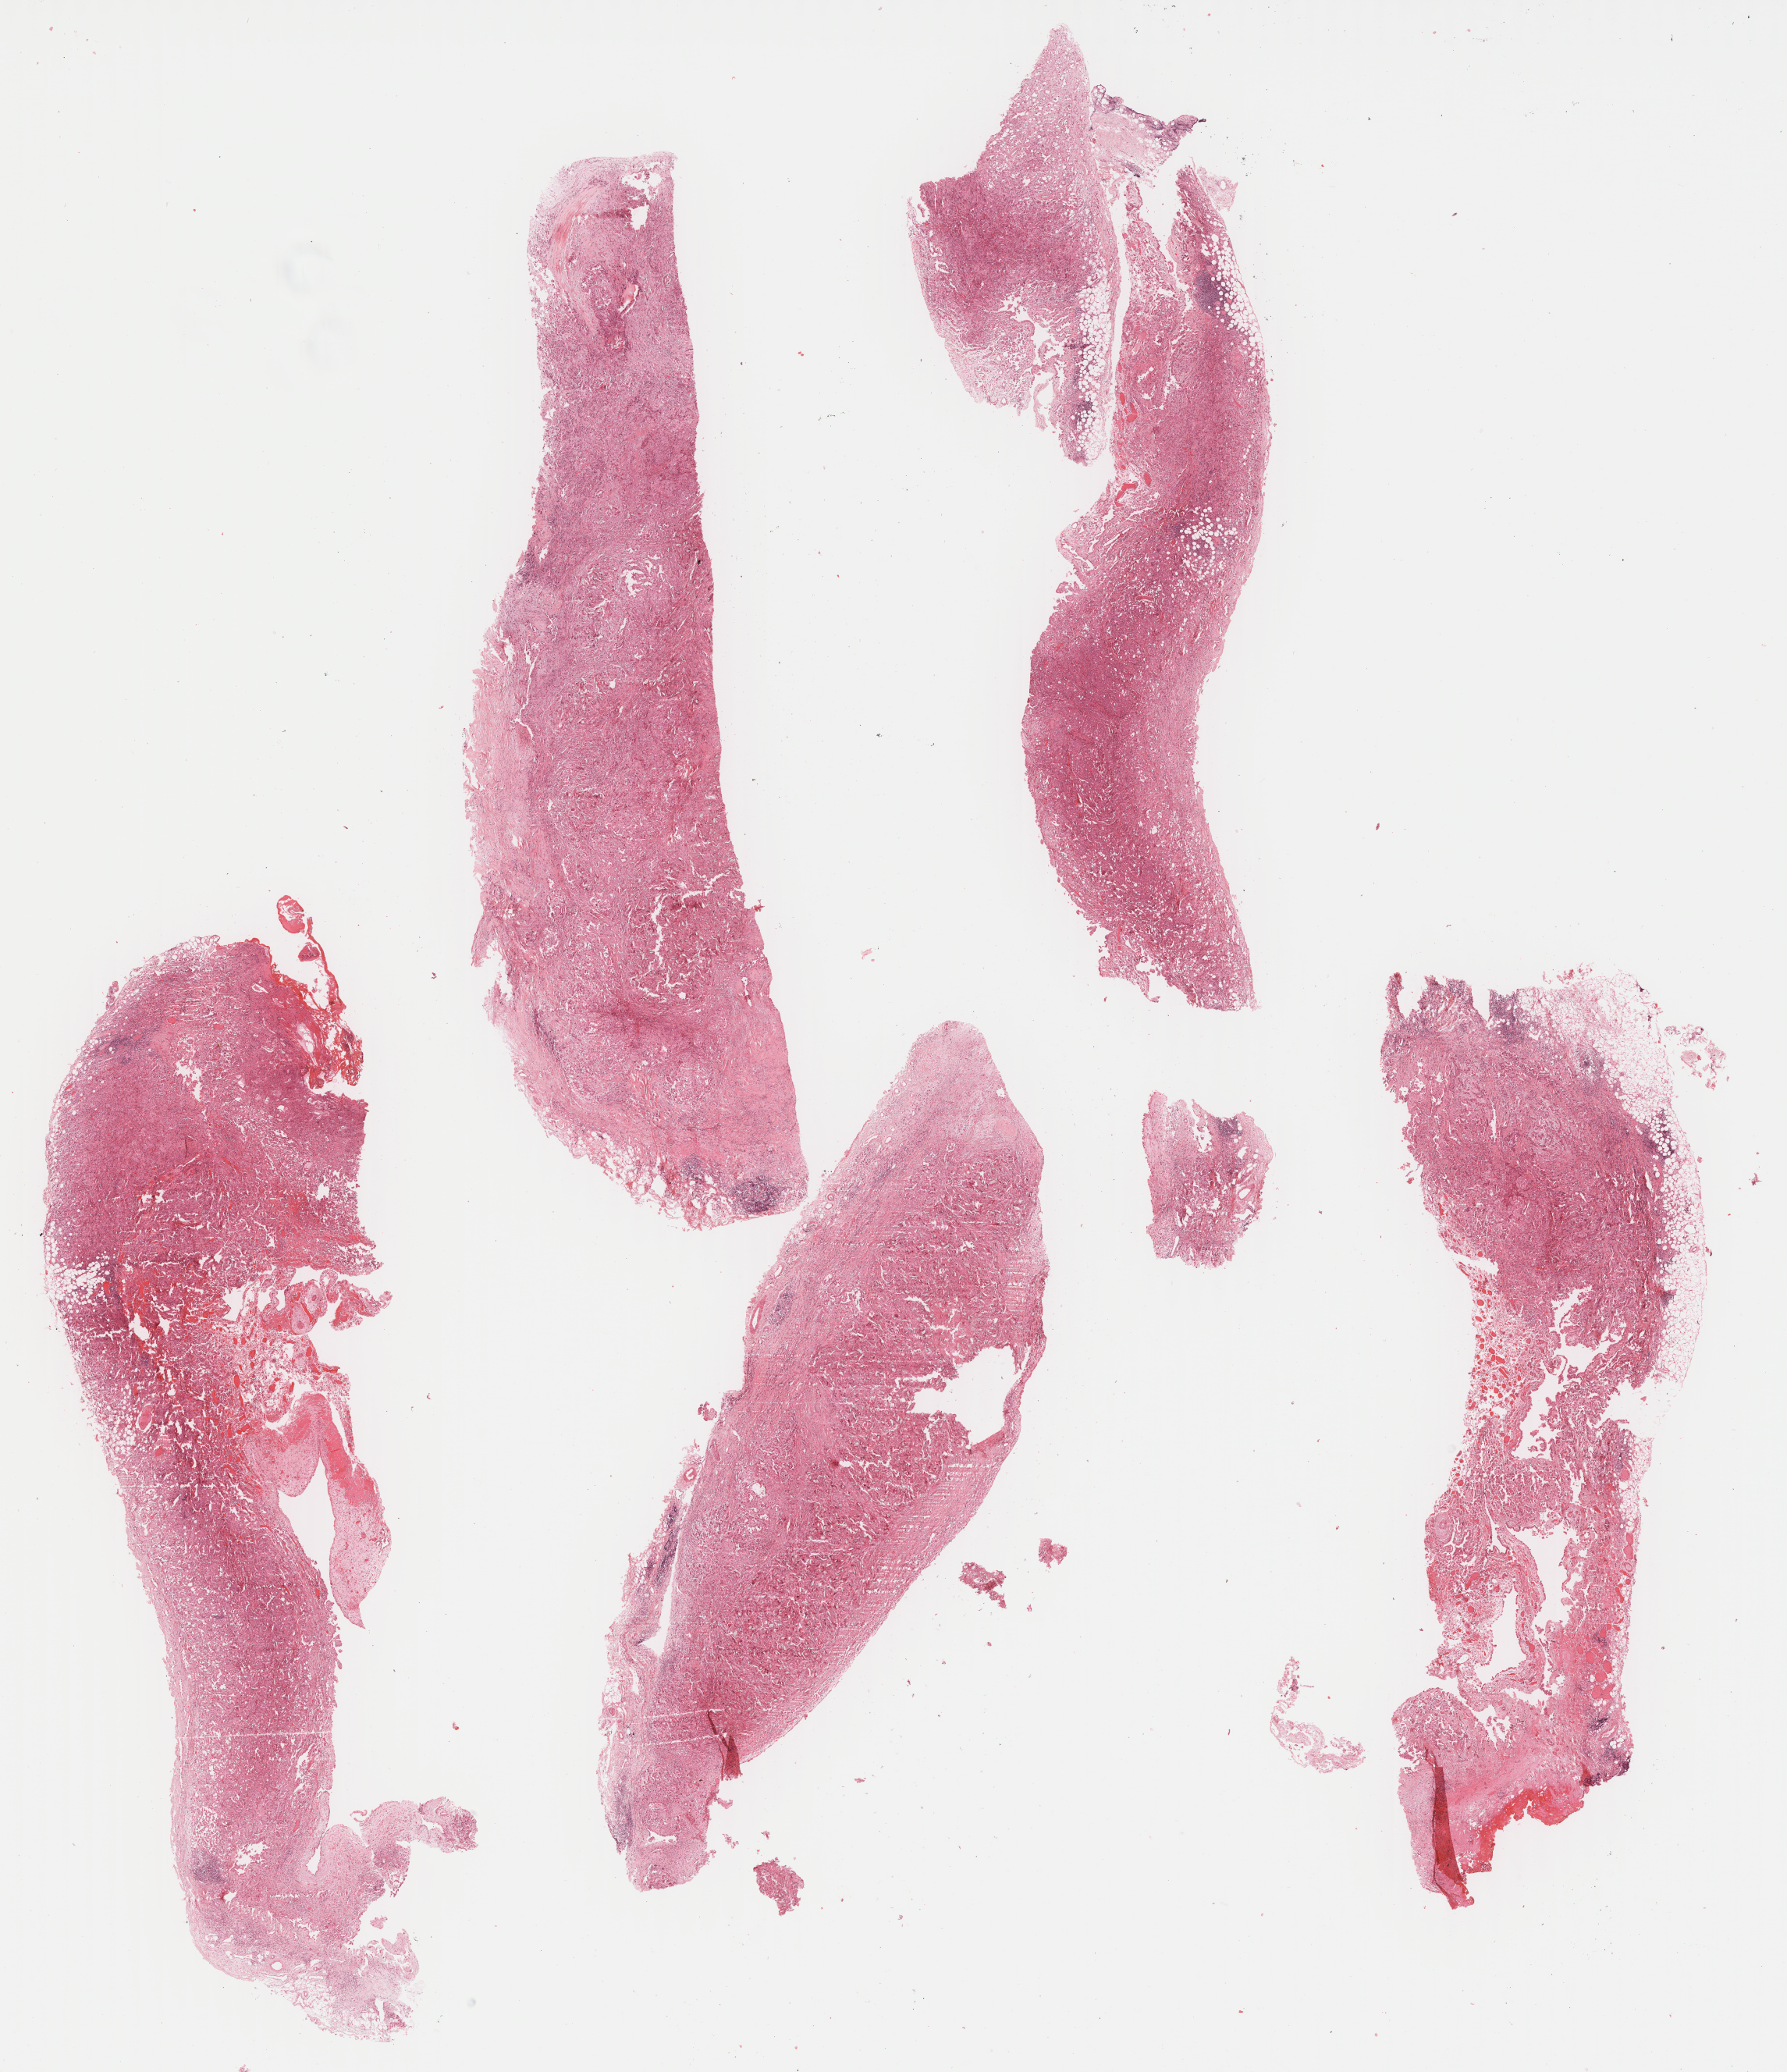
Hematoxylin and eosin (H&E) stained whole-slide image, shown as a low-resolution overview of the whole scanned area (about 18.1 x 21.0 mm); formalin-fixed paraffin-embedded (FFPE) diagnostic section; primary tumour sample from the mesothelium. Male, age 67 years at initial diagnosis.
Laterality: left. AJCC pathologic stage: II (6th edition). Pathologic diagnosis: Mesothelioma, biphasic, malignant (pleura, NOS).